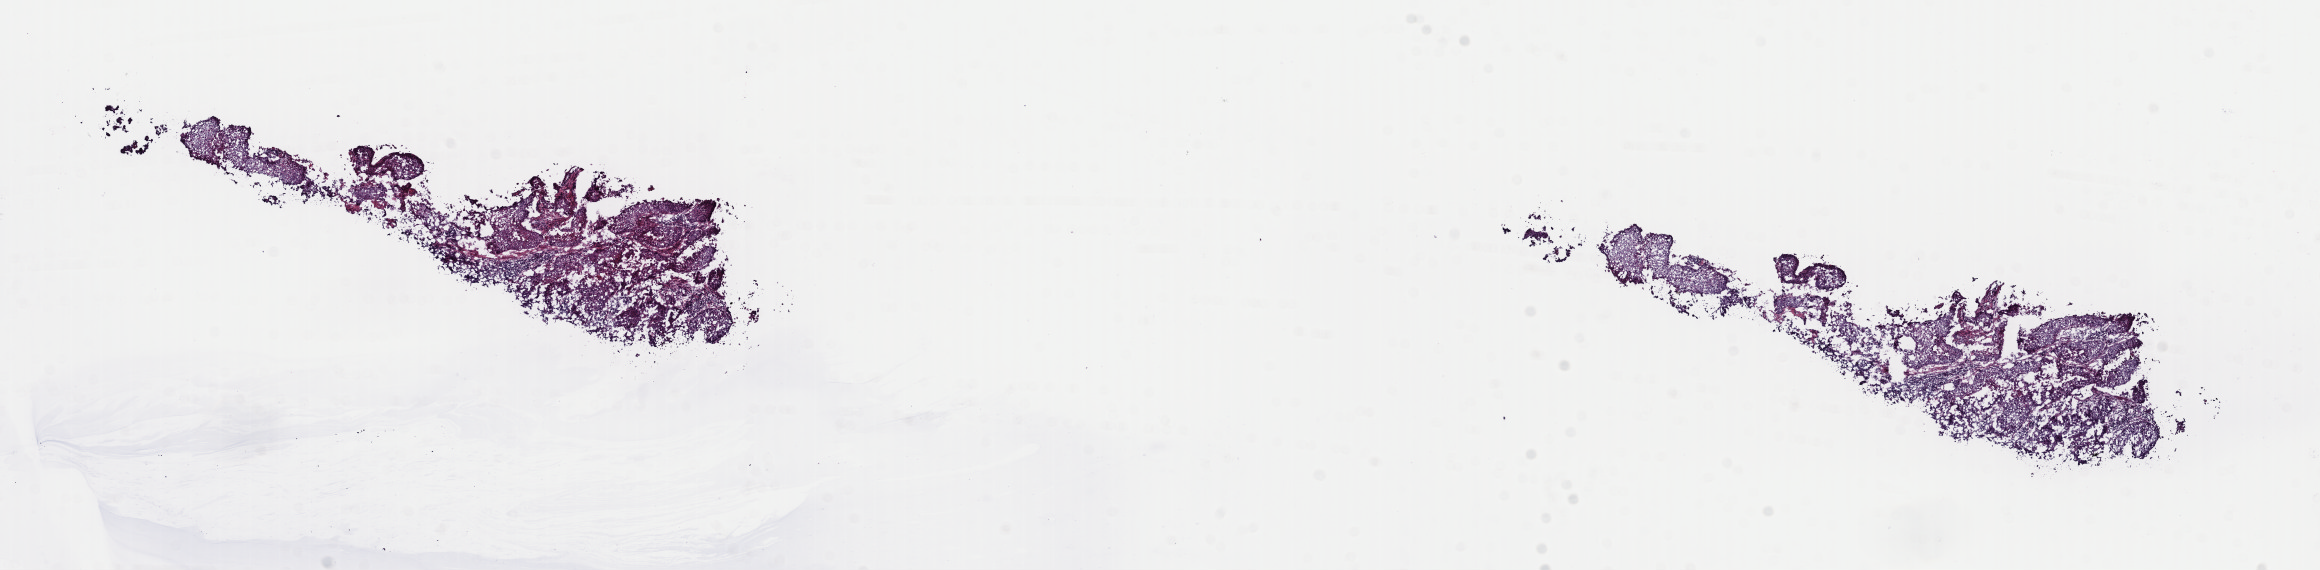
Whole-slide histology image, H&E, low-resolution overview of the scanned area, about 18.3 x 4.5 mm, frozen section, sample: primary tumour, lung. Female, age 68 years at initial diagnosis. Slide review estimates, as recorded: tumour cells 93%, tumour nuclei 100%, normal cells 0%, stromal cells 5%, necrosis 2%. Infiltration values recorded for this section: lymphocyte infiltration 2%, monocyte infiltration 2%, neutrophil infiltration 2%.
• pathologic diagnosis: Squamous cell carcinoma, NOS (lower lobe, lung)
• AJCC pathologic stage: IB